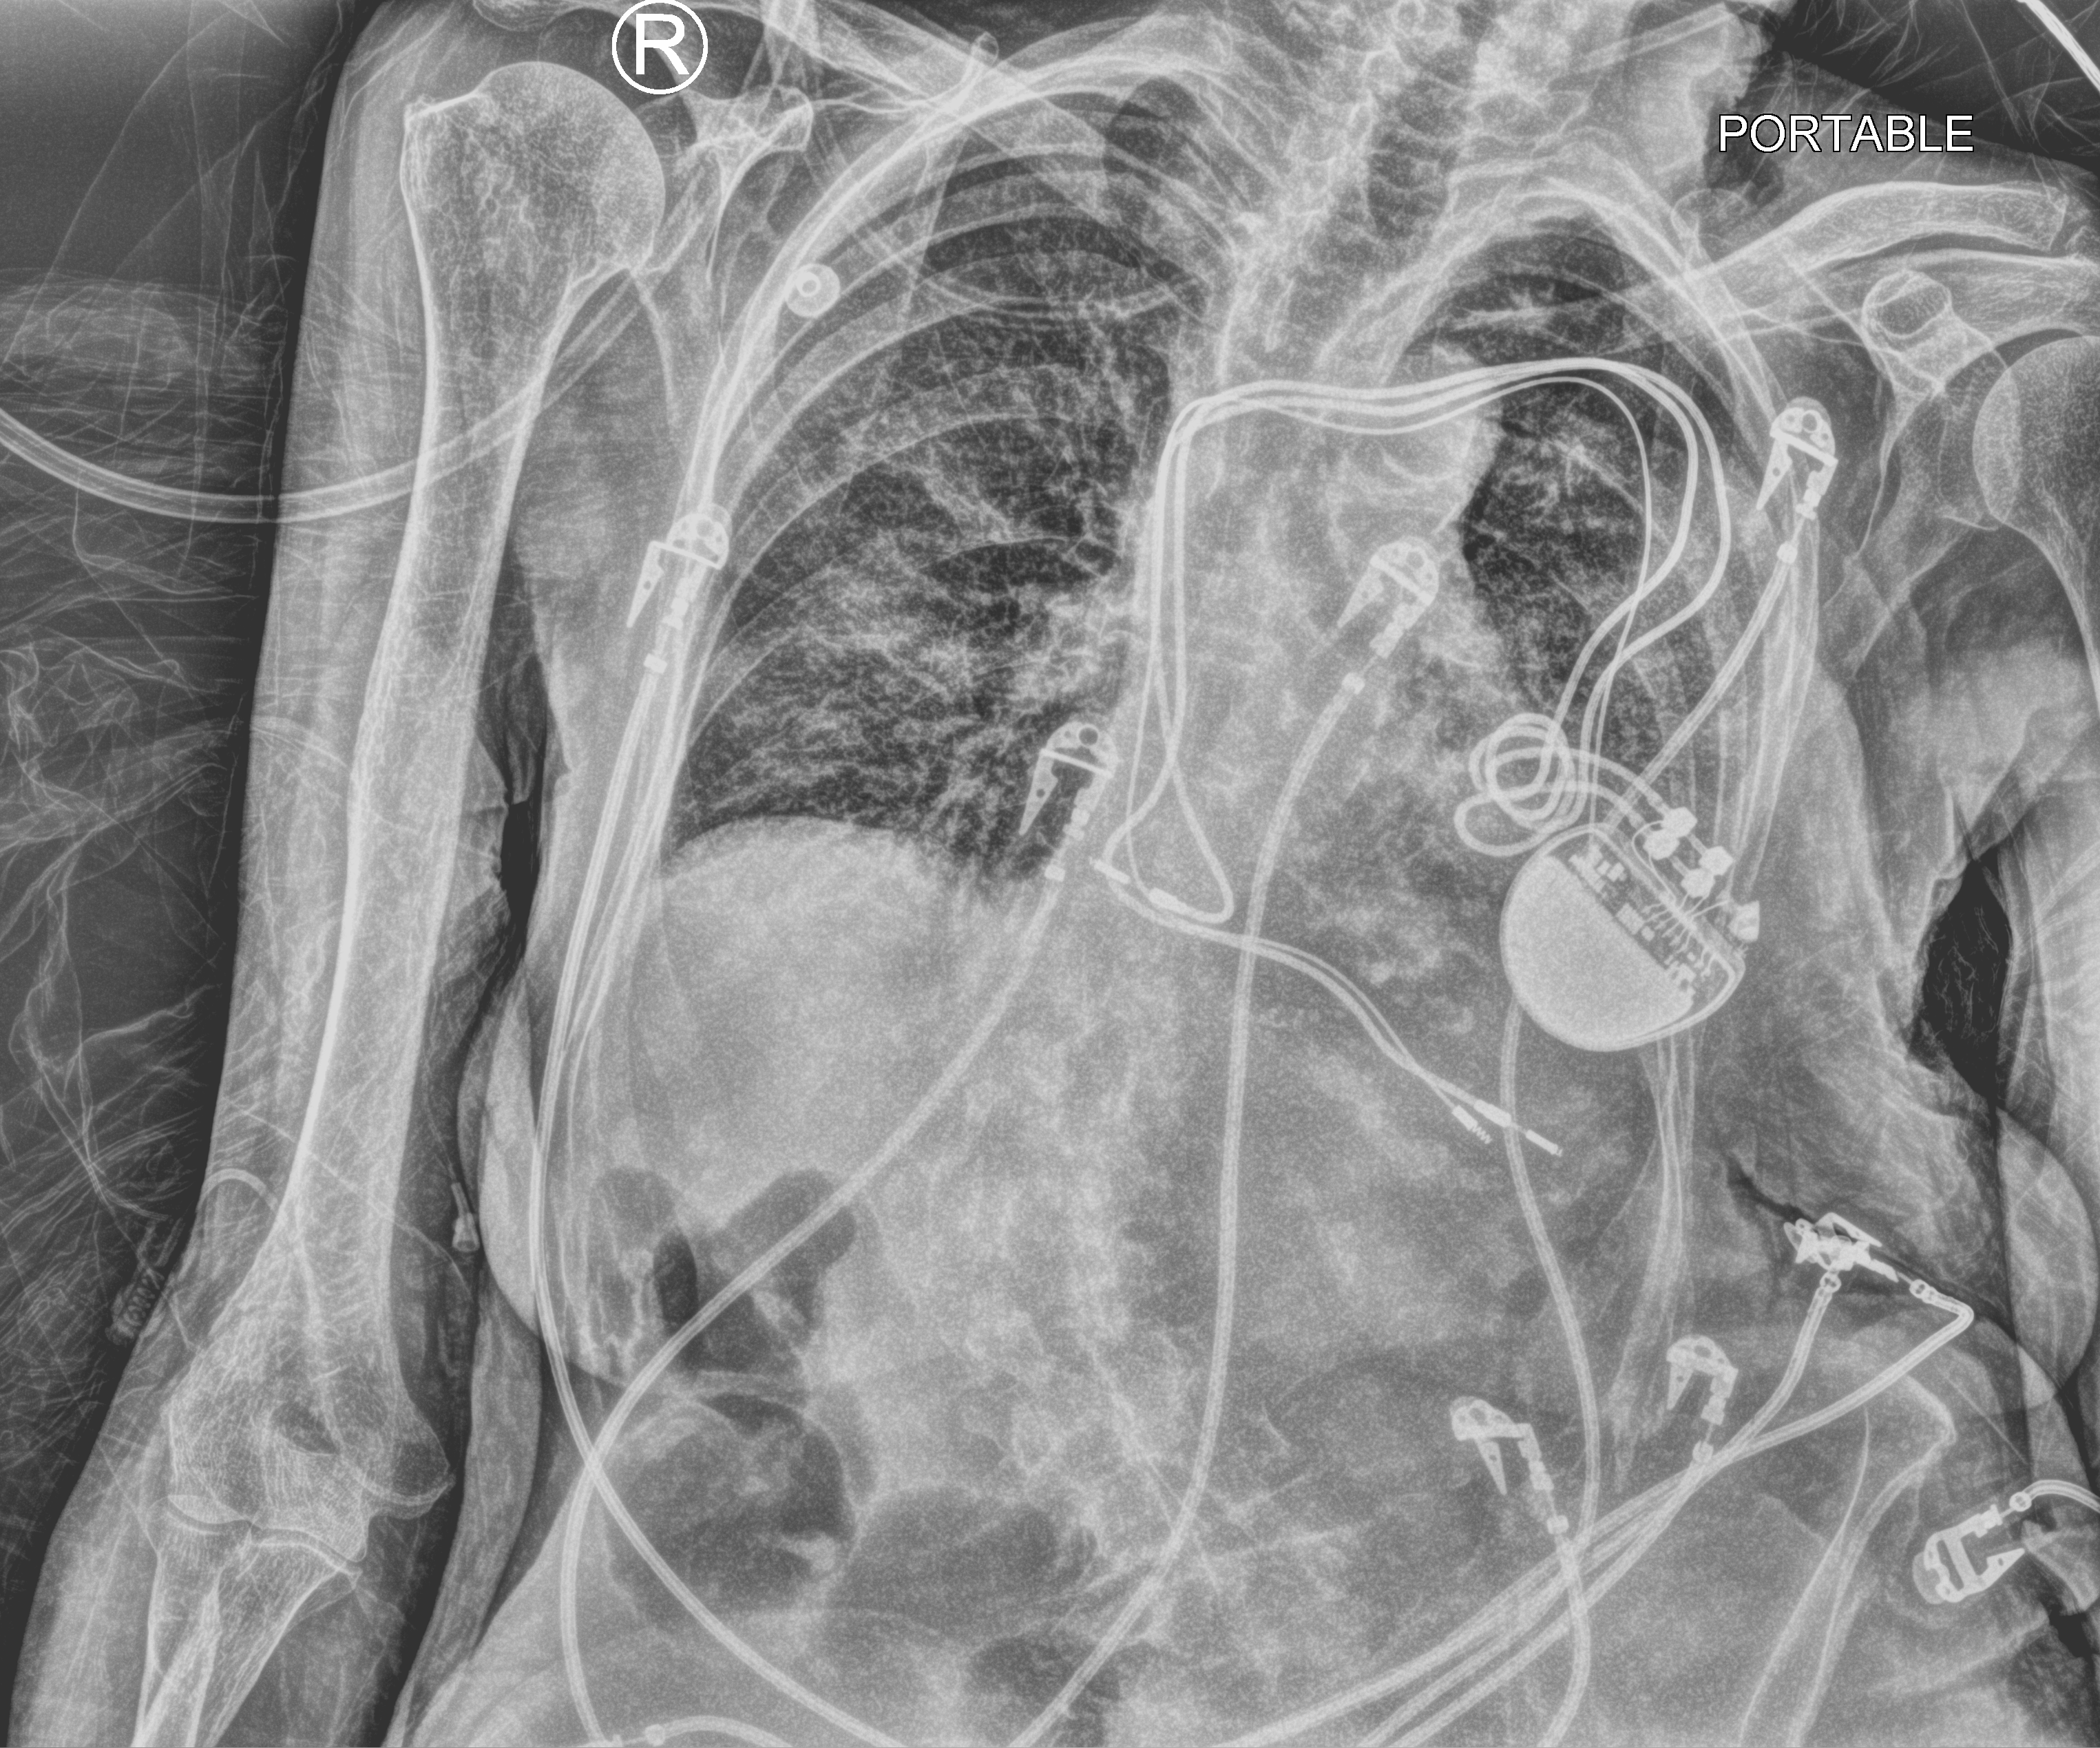
Portable chest radiograph, anteroposterior (AP) projection. Patient hospitalised with COVID-19; female, aged 75–90 years.
Hospital-stay facts (about this admission, not read from this image; timing relative to this image not recorded): mechanically ventilated during this hospital stay: no.